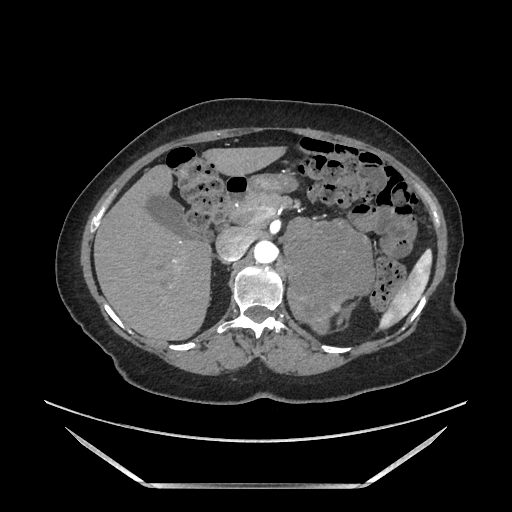
Contrast-enhanced abdominal CT, one axial slice; slice 108 of 205 in the series (ordered by position); soft-tissue window (W 400 / L 40 HU); 1.25 mm slice thickness; 512 × 512 image matrix, field of view 440 × 440 mm. Female patient. From the clinical record (not read from this slice): diagnosis: adrenocortical carcinoma; tumour side: left adrenal.
Outlined on this slice (semi-automatically segmented with operator editing):
- mass: box from (x=286, y=220) to (x=373, y=332) px